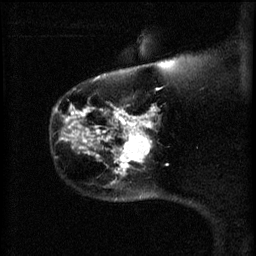
Breast MRI (dynamic contrast-enhanced), one sagittal slice. Position 50 of 60 along the scan axis. 3 images stored at this slice position (order not interpretable as contrast timing). 1.5 T. TE 4.2 ms, TR 11 ms. 2 mm slice thickness. 256 × 256 image matrix. Female patient, age 44 years.
Annotated regions visible in this slice (semi-automatic segmentation, software-assisted and operator-edited):
- analysis volume of interest (the breast-tissue region the enhancement analysis was run in; not a lesion): box from (x=110, y=124) to (x=155, y=175) px
- tumour enhancement mask (voxels above the 70 % enhancement threshold inside the analysis volume of interest): (x=116, y=124)–(x=153, y=175)